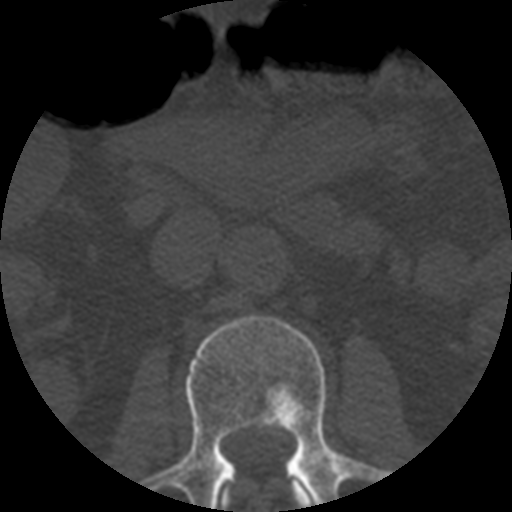
CT including the spine, one axial slice. Reconstruction kernel STANDARD. Bone window (W 1800 / L 400 HU). 1.25 mm slice thickness. 512 × 512 image matrix. Patient age 57 years. Case-level facts recorded for this patient, not image findings: primary cancer: prostate.
Annotated regions visible in this slice (semi-automatic segmentation, software-assisted and operator-edited):
- L1 vertebra: box from (x=219, y=483) to (x=314, y=509) px
- L2 vertebra: (x=140, y=316)–(x=390, y=512)